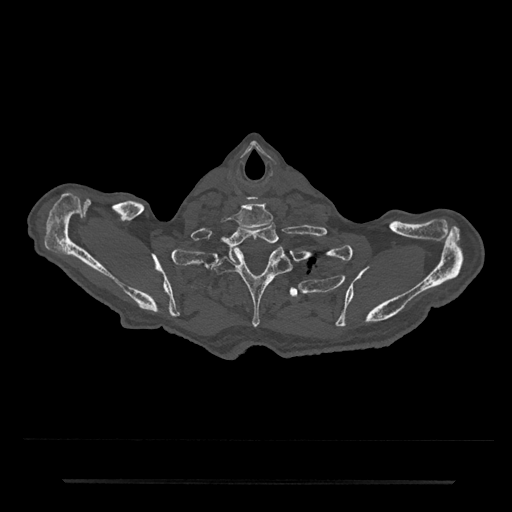
CT including the spine, one axial slice; position 705 of 797 along the scan axis; reconstruction kernel Br40s/3; bone window (W 1800 / L 400 HU); 0.5 mm slice thickness; 512 × 512 image matrix. Patient: male, 74 years. Case-level facts recorded for this patient, not image findings: primary cancer: prostate.
Outlined on this slice (semi-automatic segmentation, software-assisted and operator-edited):
- T1 vertebra: bounding box <227,223,278,257> (left, top, right, bottom; pixels)
- T2 vertebra: <212,248,291,329>
- T3 vertebra: <217,287,299,299>